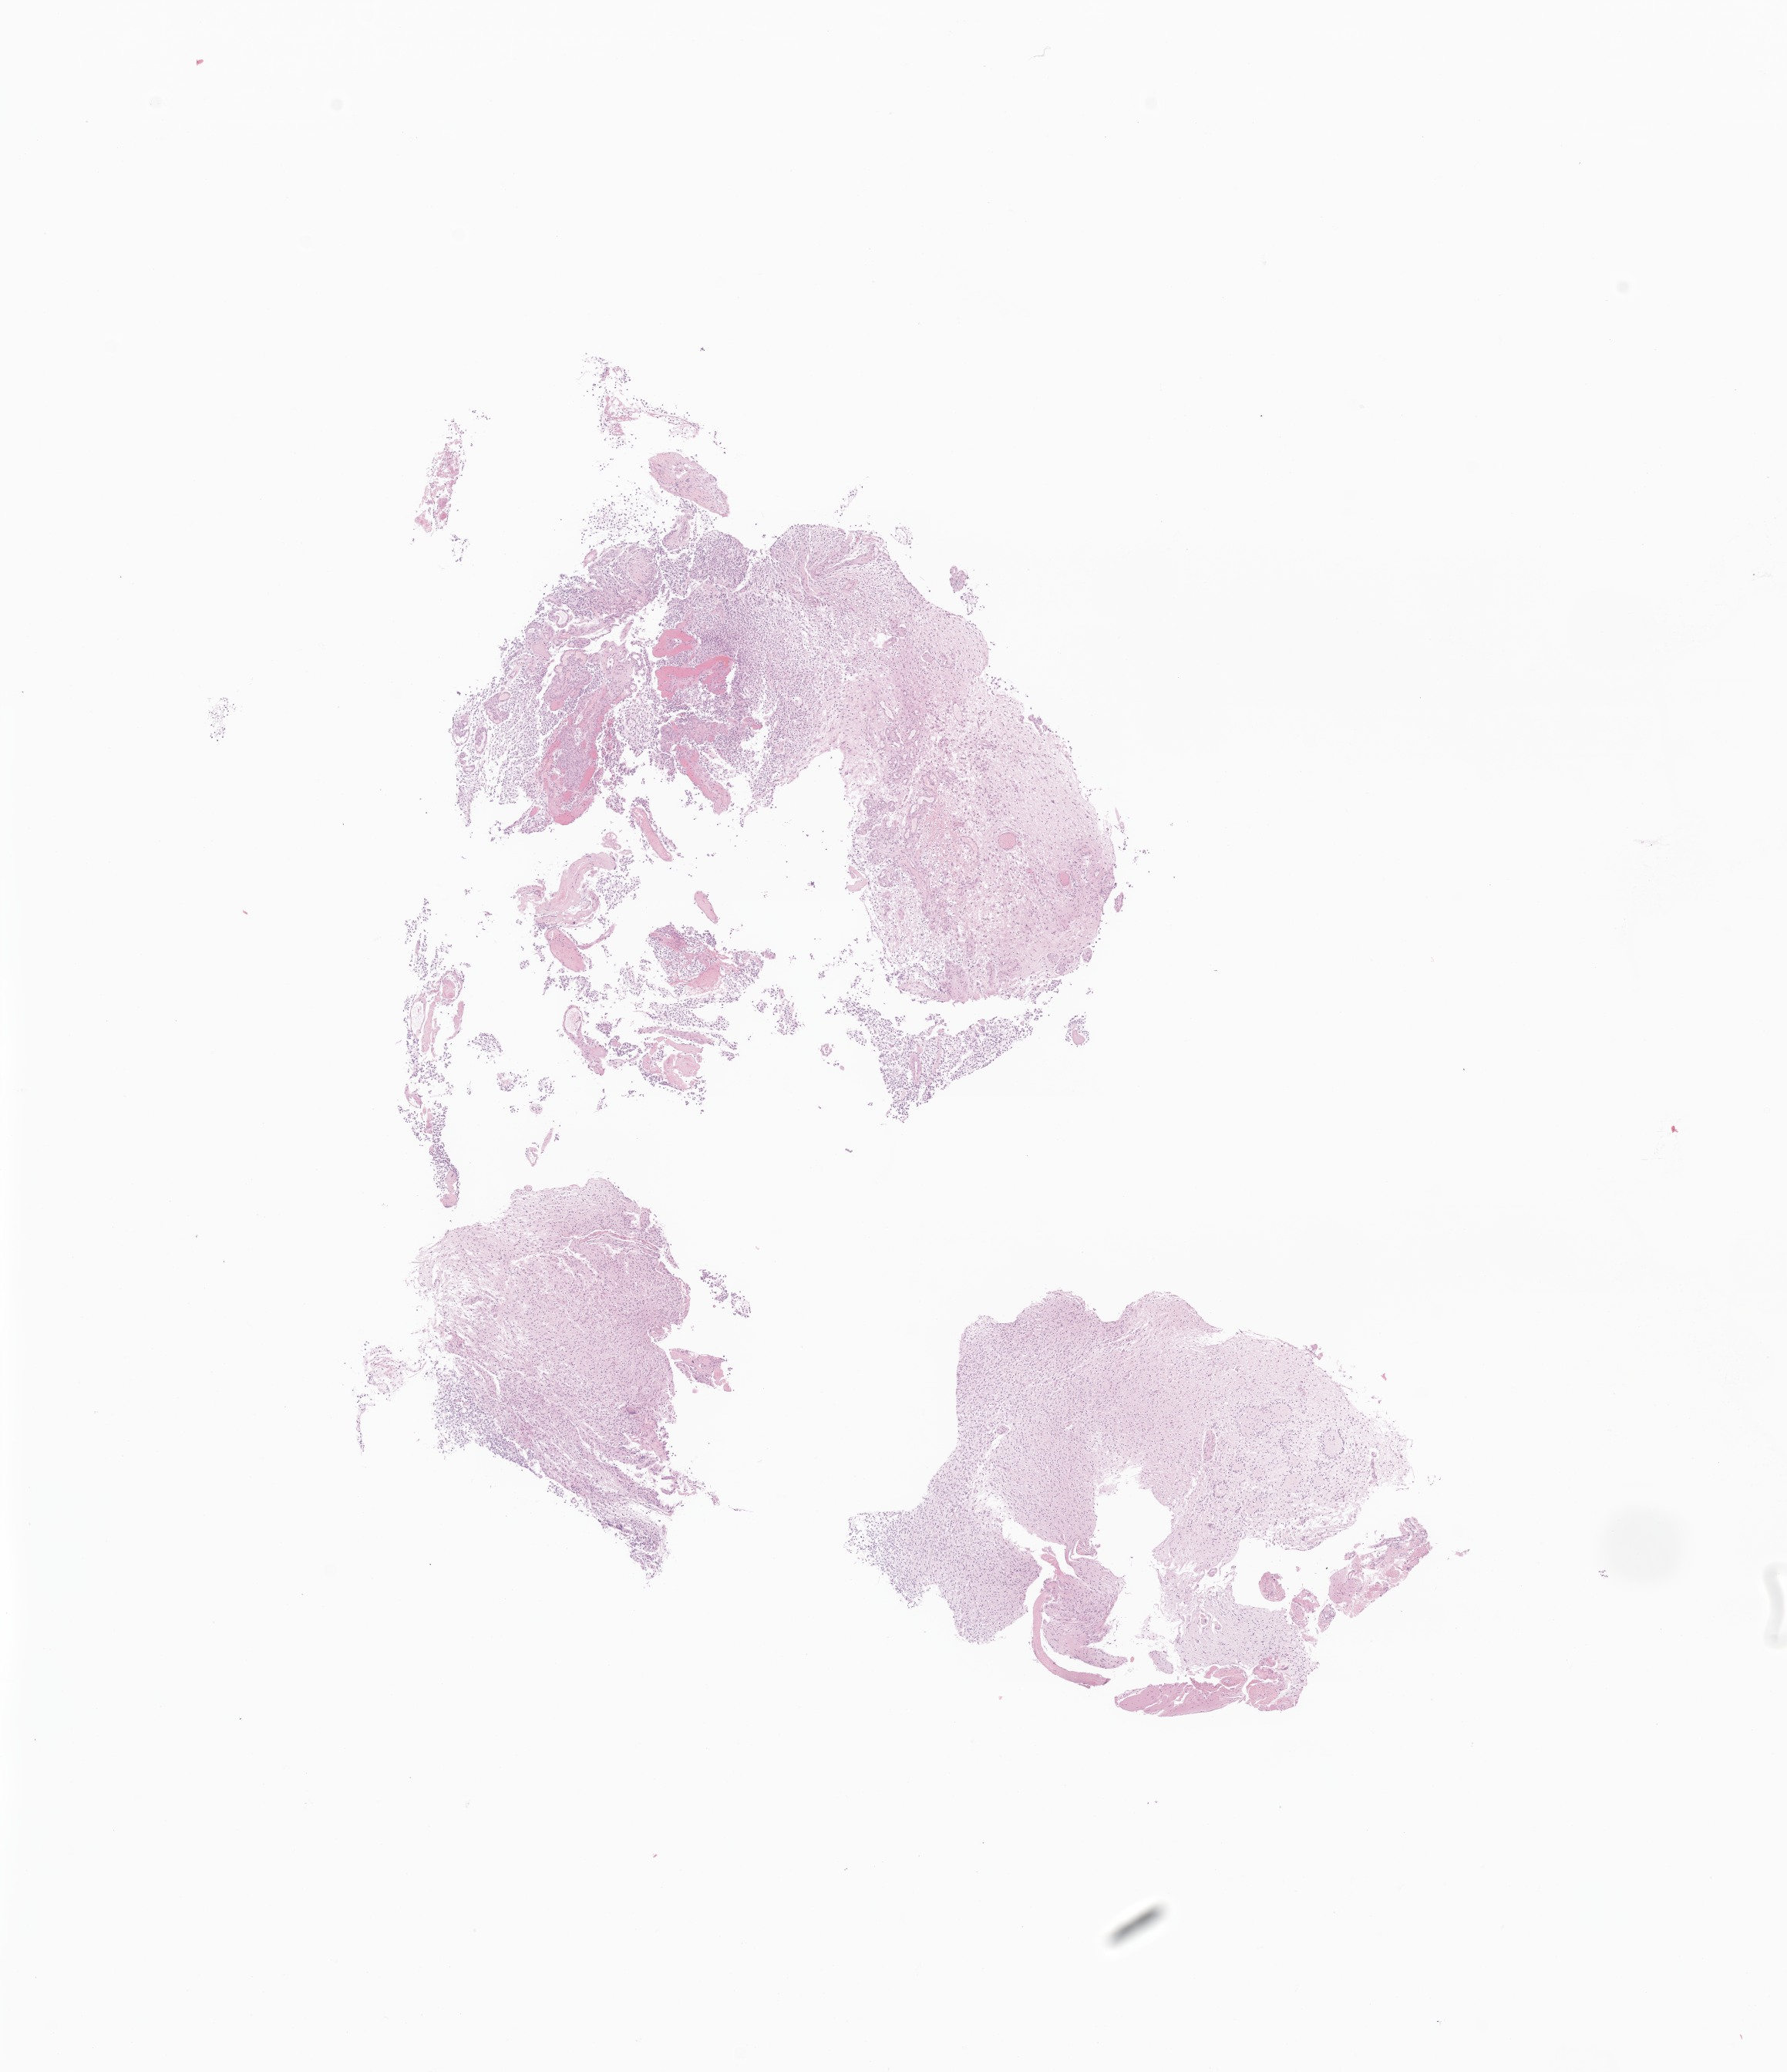
Digitized haematoxylin and eosin-stained section of tumor tissue from the spinal cord — a low-resolution overview of the entire scanned area, about 9.8 x 11.3 mm. Formalin-fixed, paraffin-embedded (FFPE) tissue. Patient male; age 37 months (3 years 1 month).
Diagnosis: Glioma, malignant.